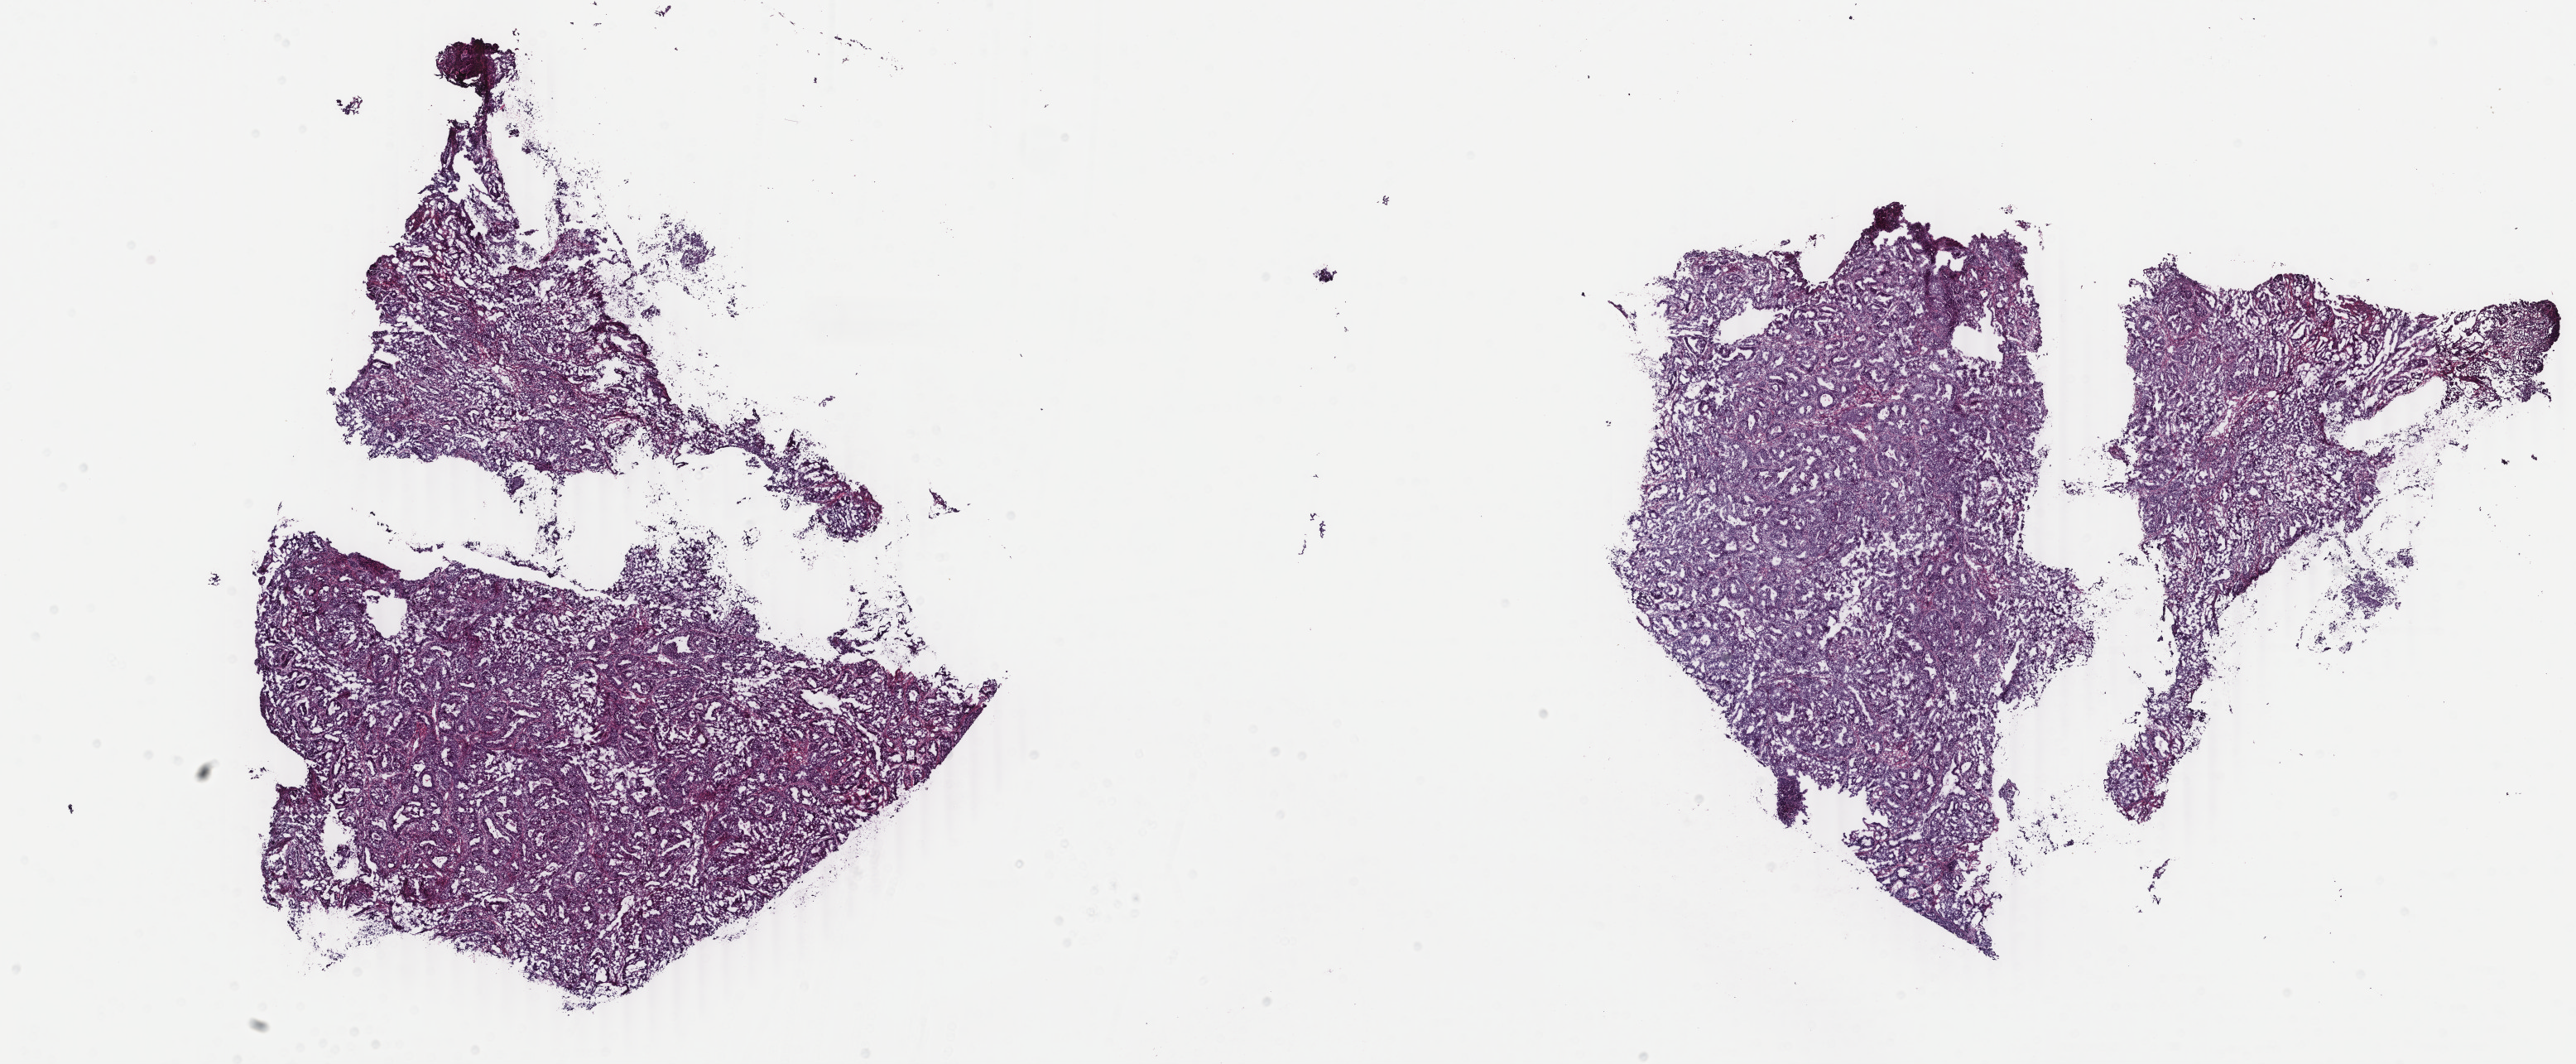
Digitized H&E-stained tissue section (whole slide), low-resolution overview of the scanned area, about 24.7 x 10.2 mm (acquisition: 40x scan). Frozen section from the top of the tissue portion. Primary tumour sample from the uterus. Patient: female, age at initial diagnosis 57 years.
Histologic diagnosis: Endometrioid adenocarcinoma, NOS (endometrium).